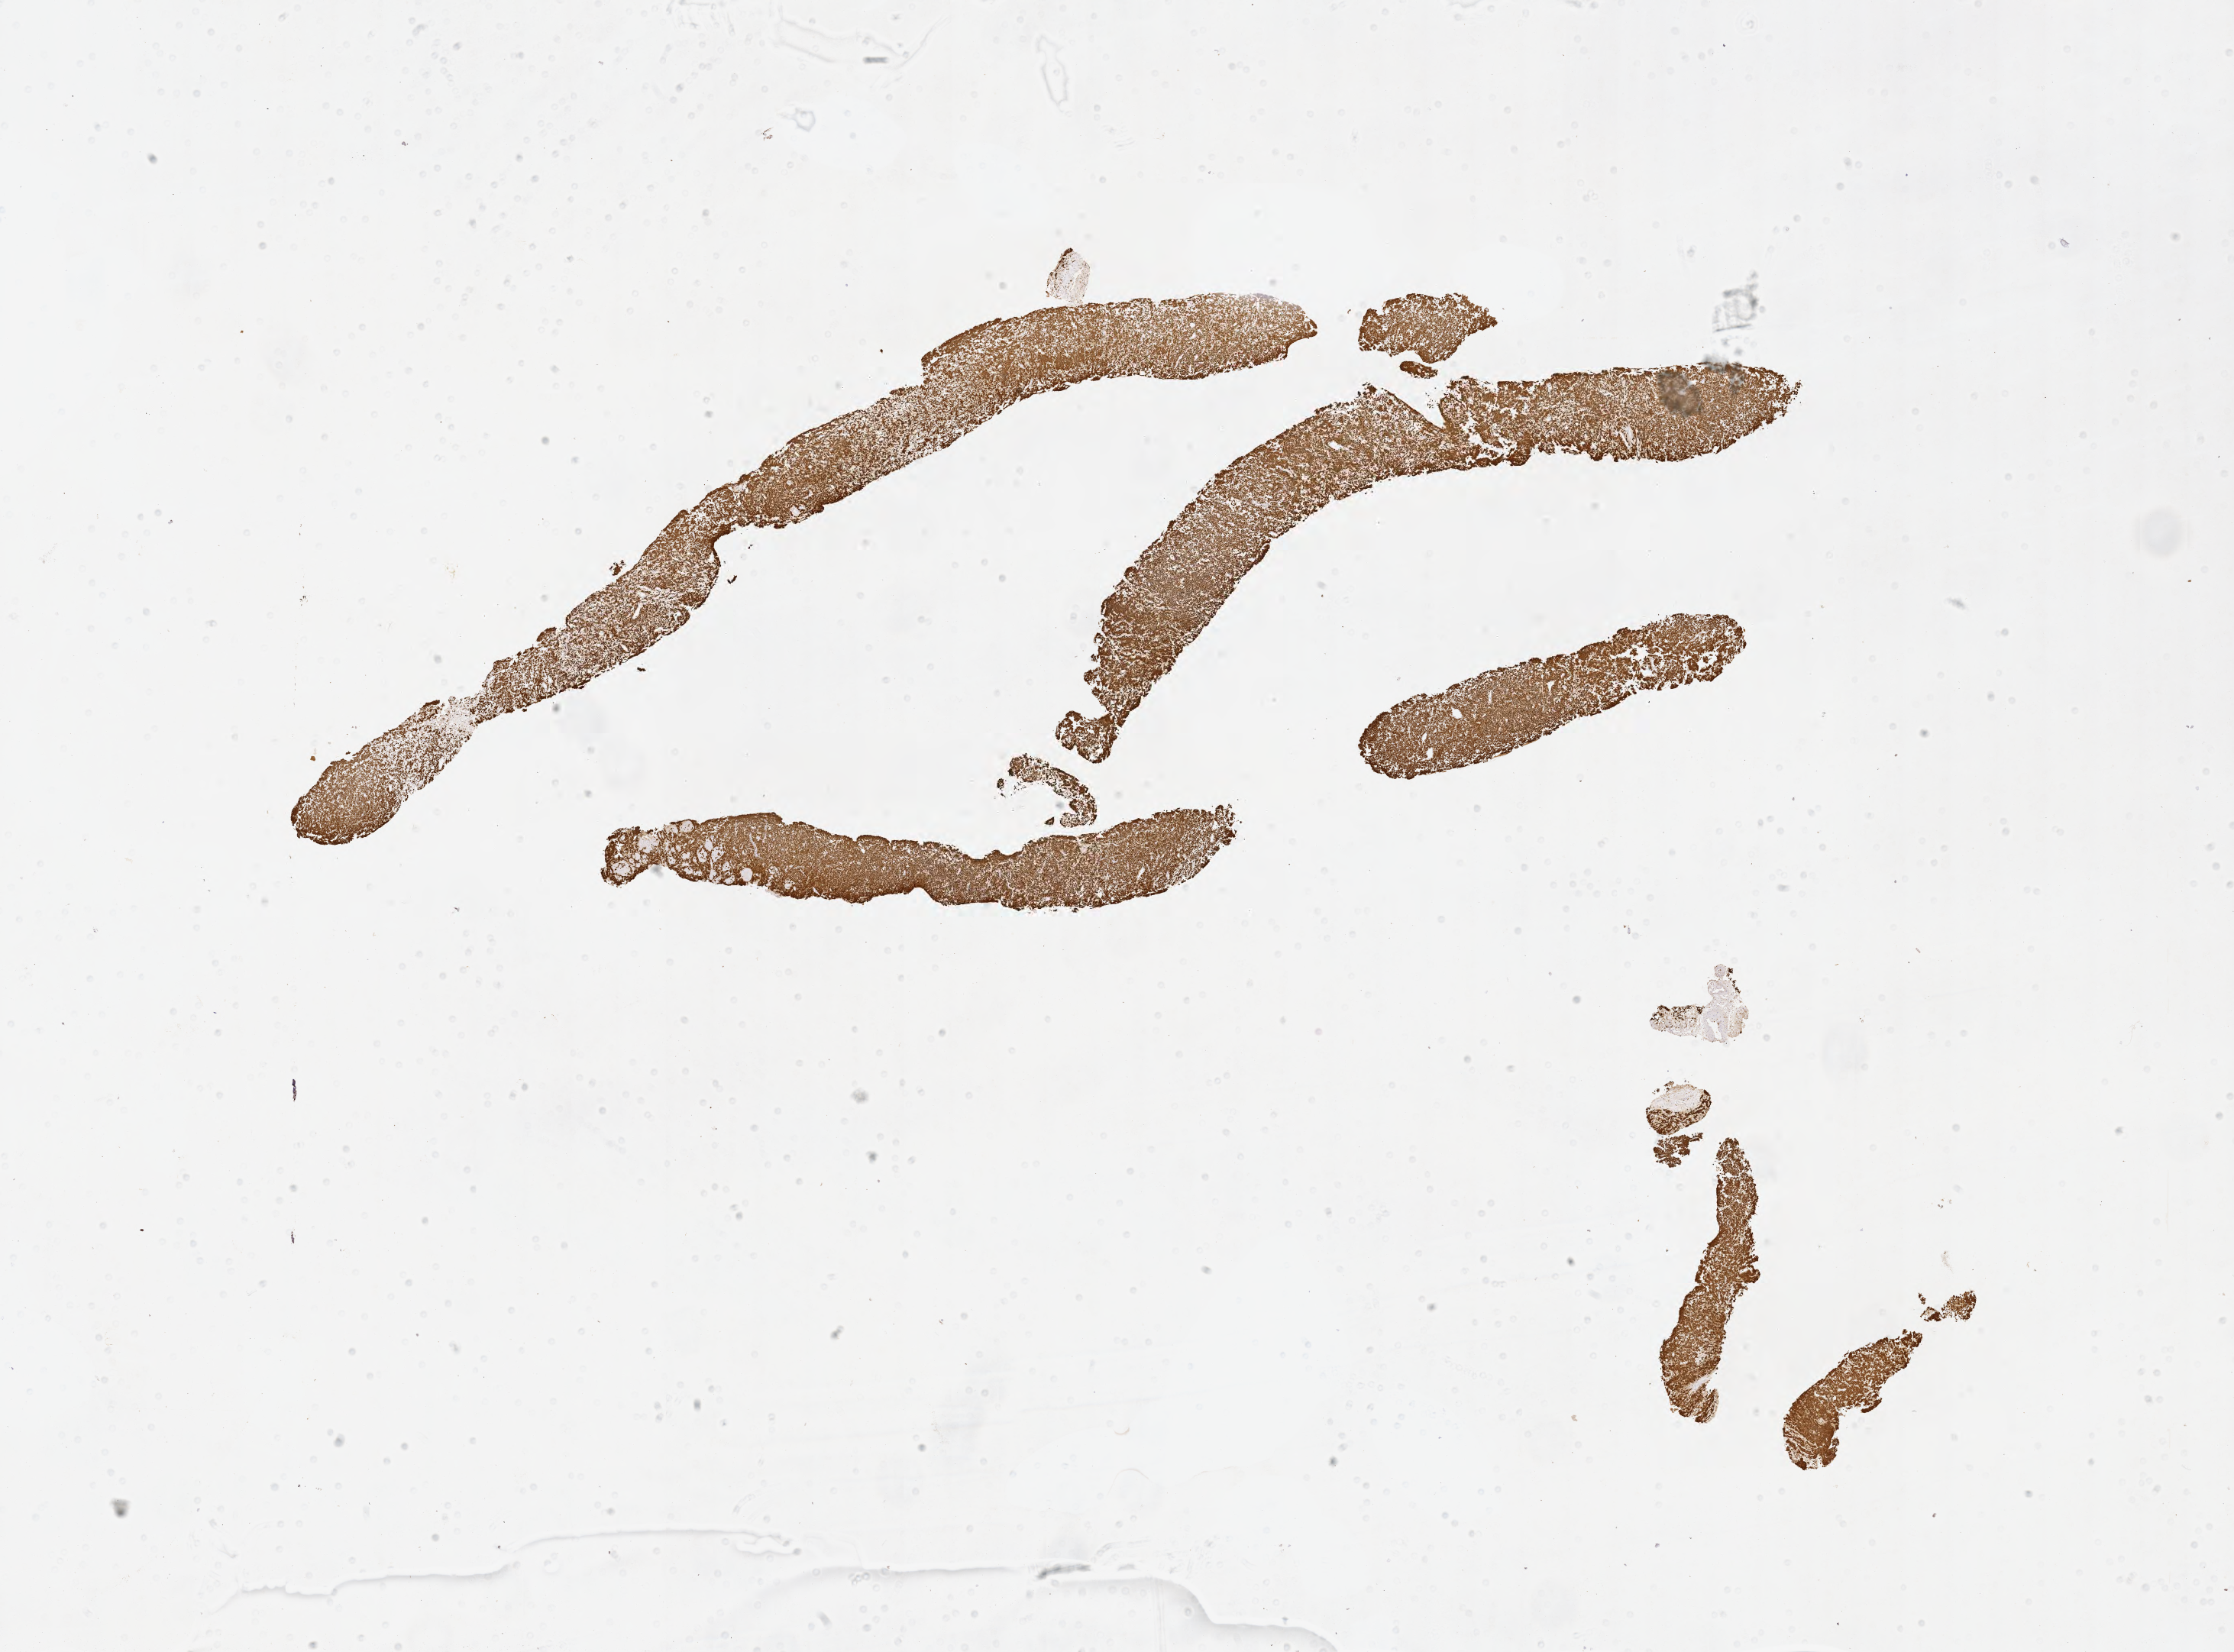
Whole-slide image, immunohistochemical stain for Ki-67, whole scanned area (about 23.6 x 17.5 mm) shown as a low-resolution overview, tumor tissue. Male patient, aged 66.
Histologic diagnosis: Burkitt lymphoma, NOS.